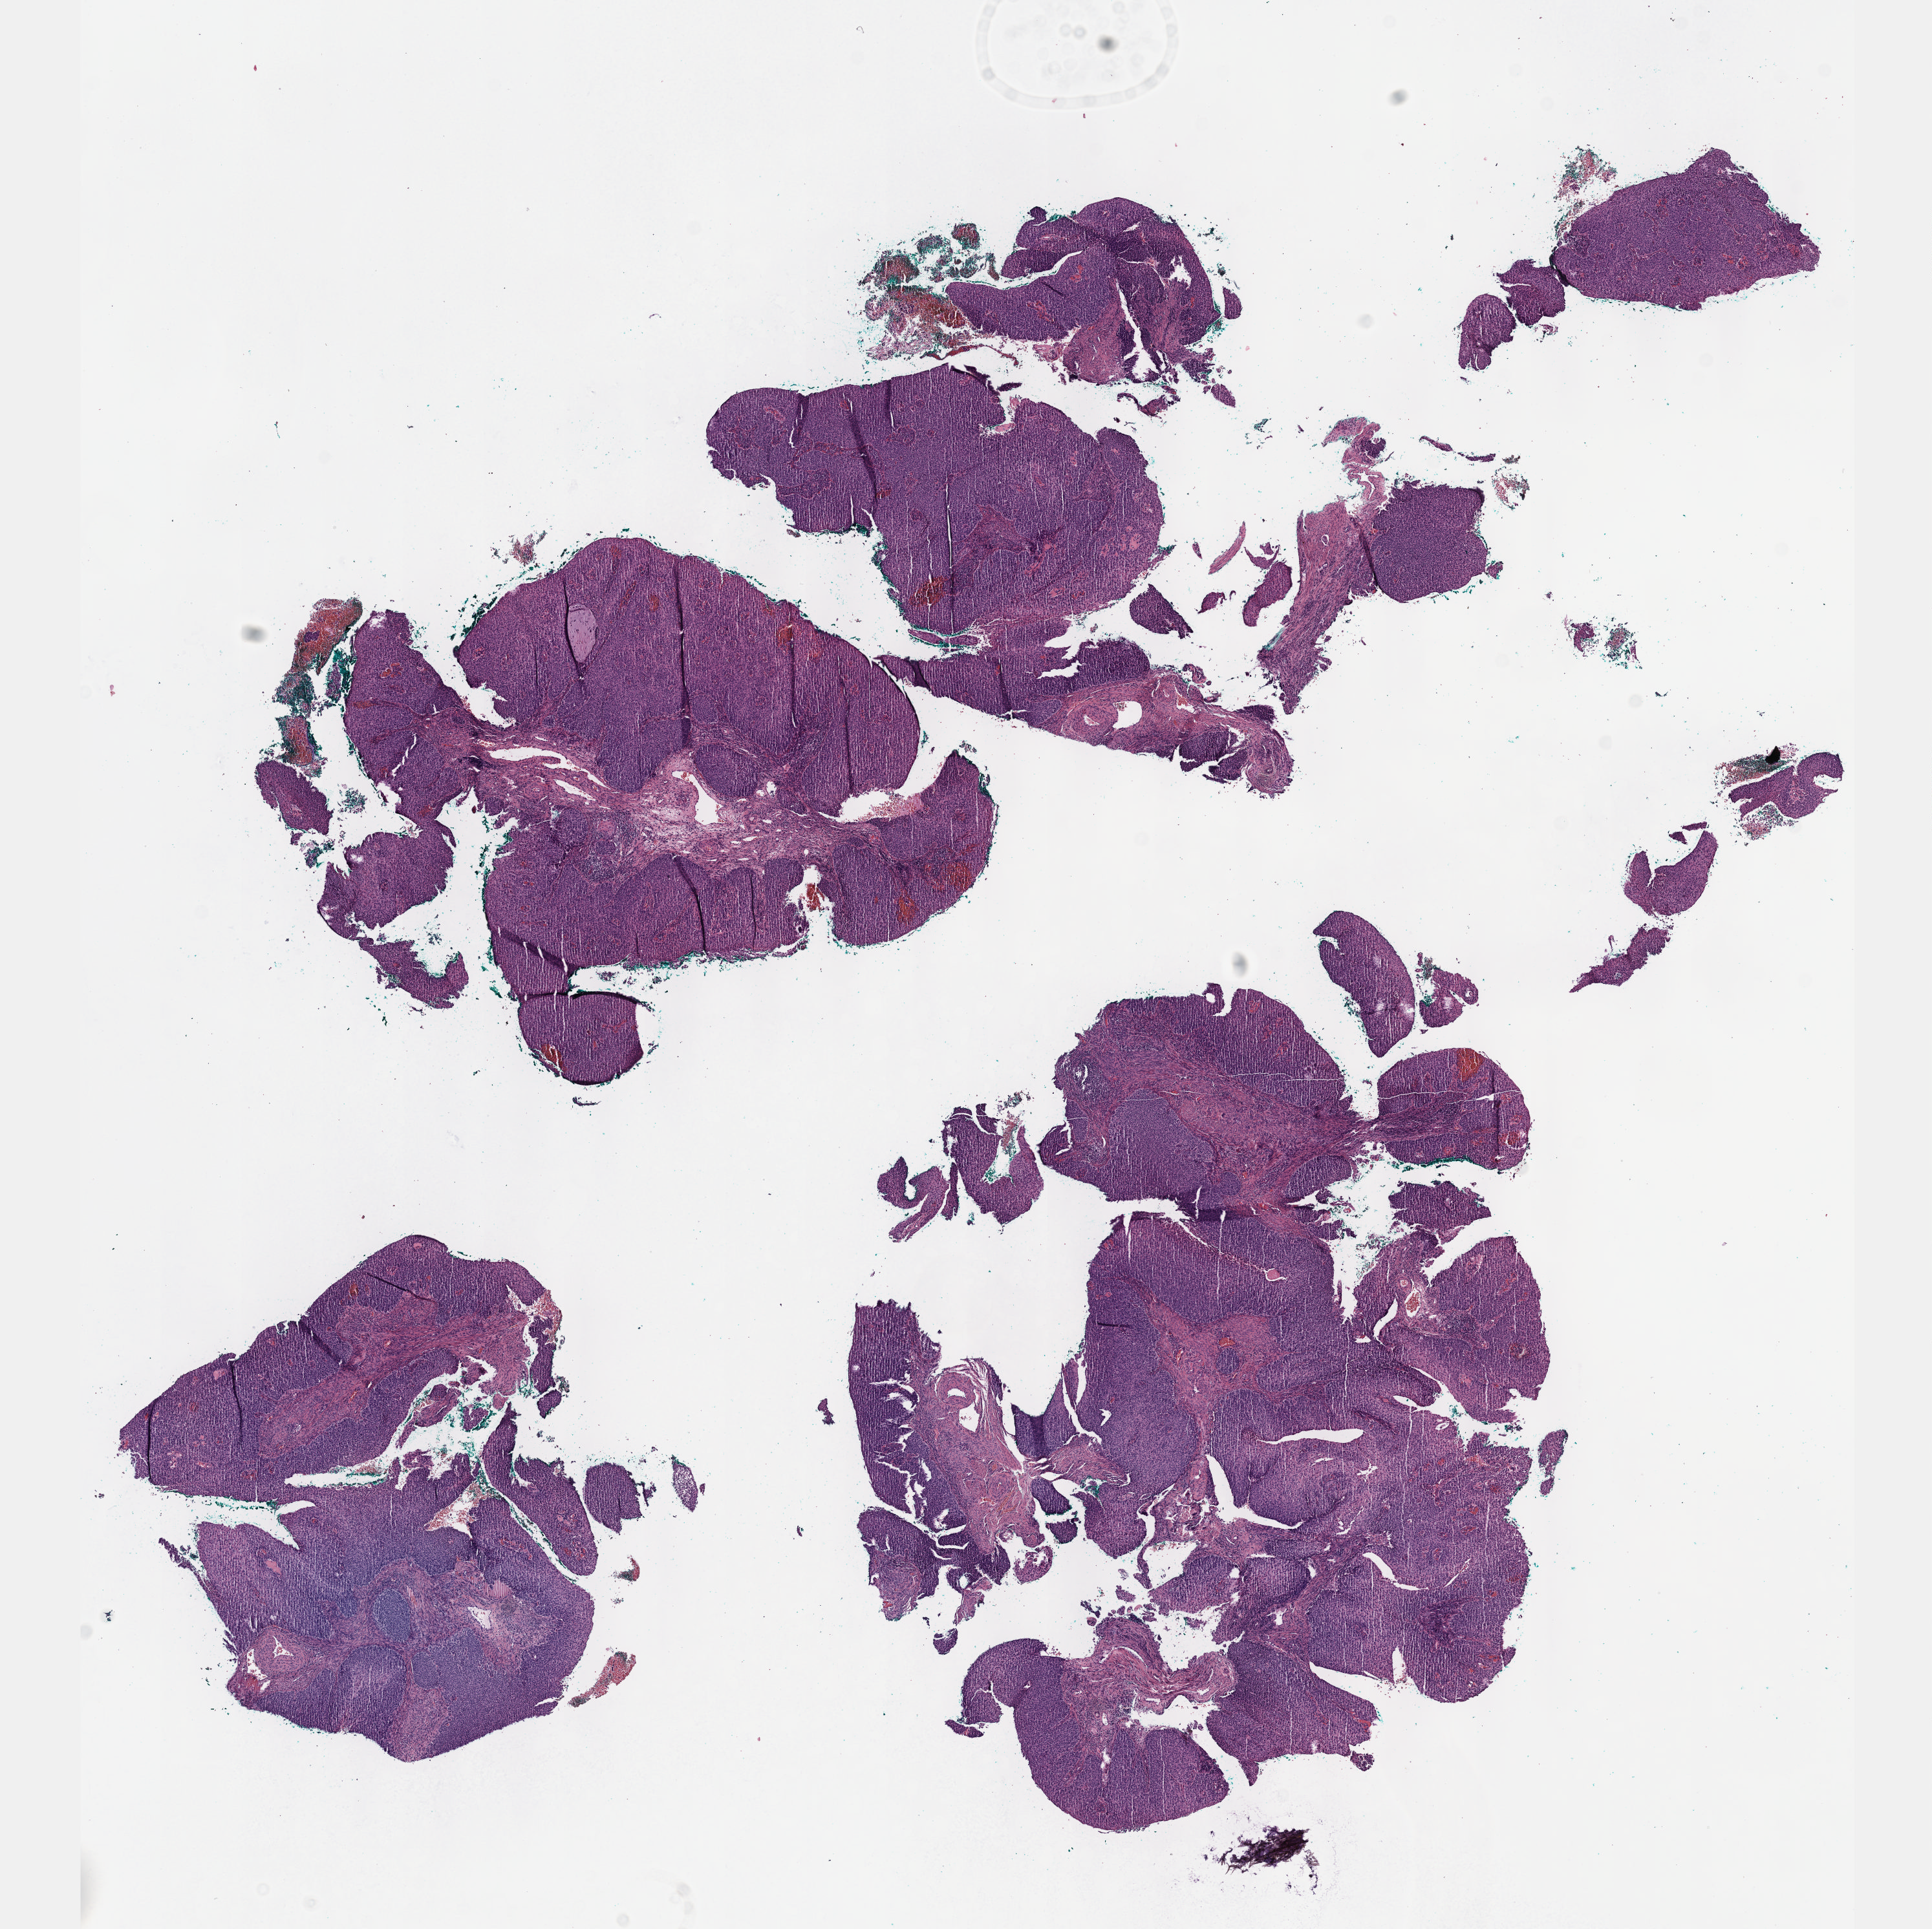
Digitized H&E tissue section (whole slide) — low-resolution overview of the scanned area, about 12.1 x 12.1 mm (slide scanned at 40x). Formalin-fixed paraffin-embedded (FFPE) diagnostic section. Cervix, primary tumour sample. Female, age 36 years at initial diagnosis. Histologic grade: GX (grade cannot be assessed).
• pathologic diagnosis: Squamous cell carcinoma, NOS (cervix uteri)
• FIGO stage: IB1